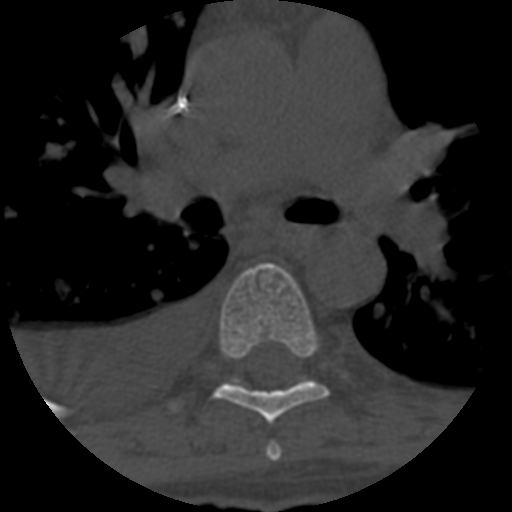
CT including the spine, one axial slice; position 434 of 708 along the scan axis; reconstruction kernel STANDARD; 120 kVp; one of 3 acquisitions stored at this slice position; bone window (W 1800 / L 400 HU); 512 × 512 image matrix, field of view 160 × 160 mm. Patient age 55 years. Case-level facts recorded for this patient, not image findings: primary cancer: colon; vertebrae with lytic lesions (as recorded): T12, L1, L5.
Structures marked on this image (semi-automatically segmented with operator editing):
- T5 vertebra: bounding box [x1, y1, x2, y2] px = [266, 443, 282, 461]
- T6 vertebra: [214, 263, 329, 424]